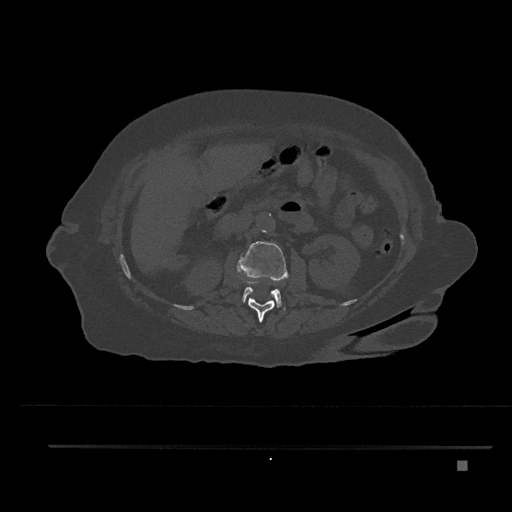
CT including the spine, one axial slice. Slice 202 of 797 in the series (ordered by position). Bone window (W 1800 / L 400 HU). 0.5 mm slice thickness. 512 × 512 image matrix, field of view 437 × 437 mm. Patient: female, 76 years. From the clinical record (not read from this slice): primary cancer: lung.
Annotated regions visible in this slice (semi-automatic segmentation, software-assisted and operator-edited):
- L1 vertebra: bounding box [x1, y1, x2, y2] px = [241, 280, 276, 322]
- L2 vertebra: [237, 241, 289, 307]